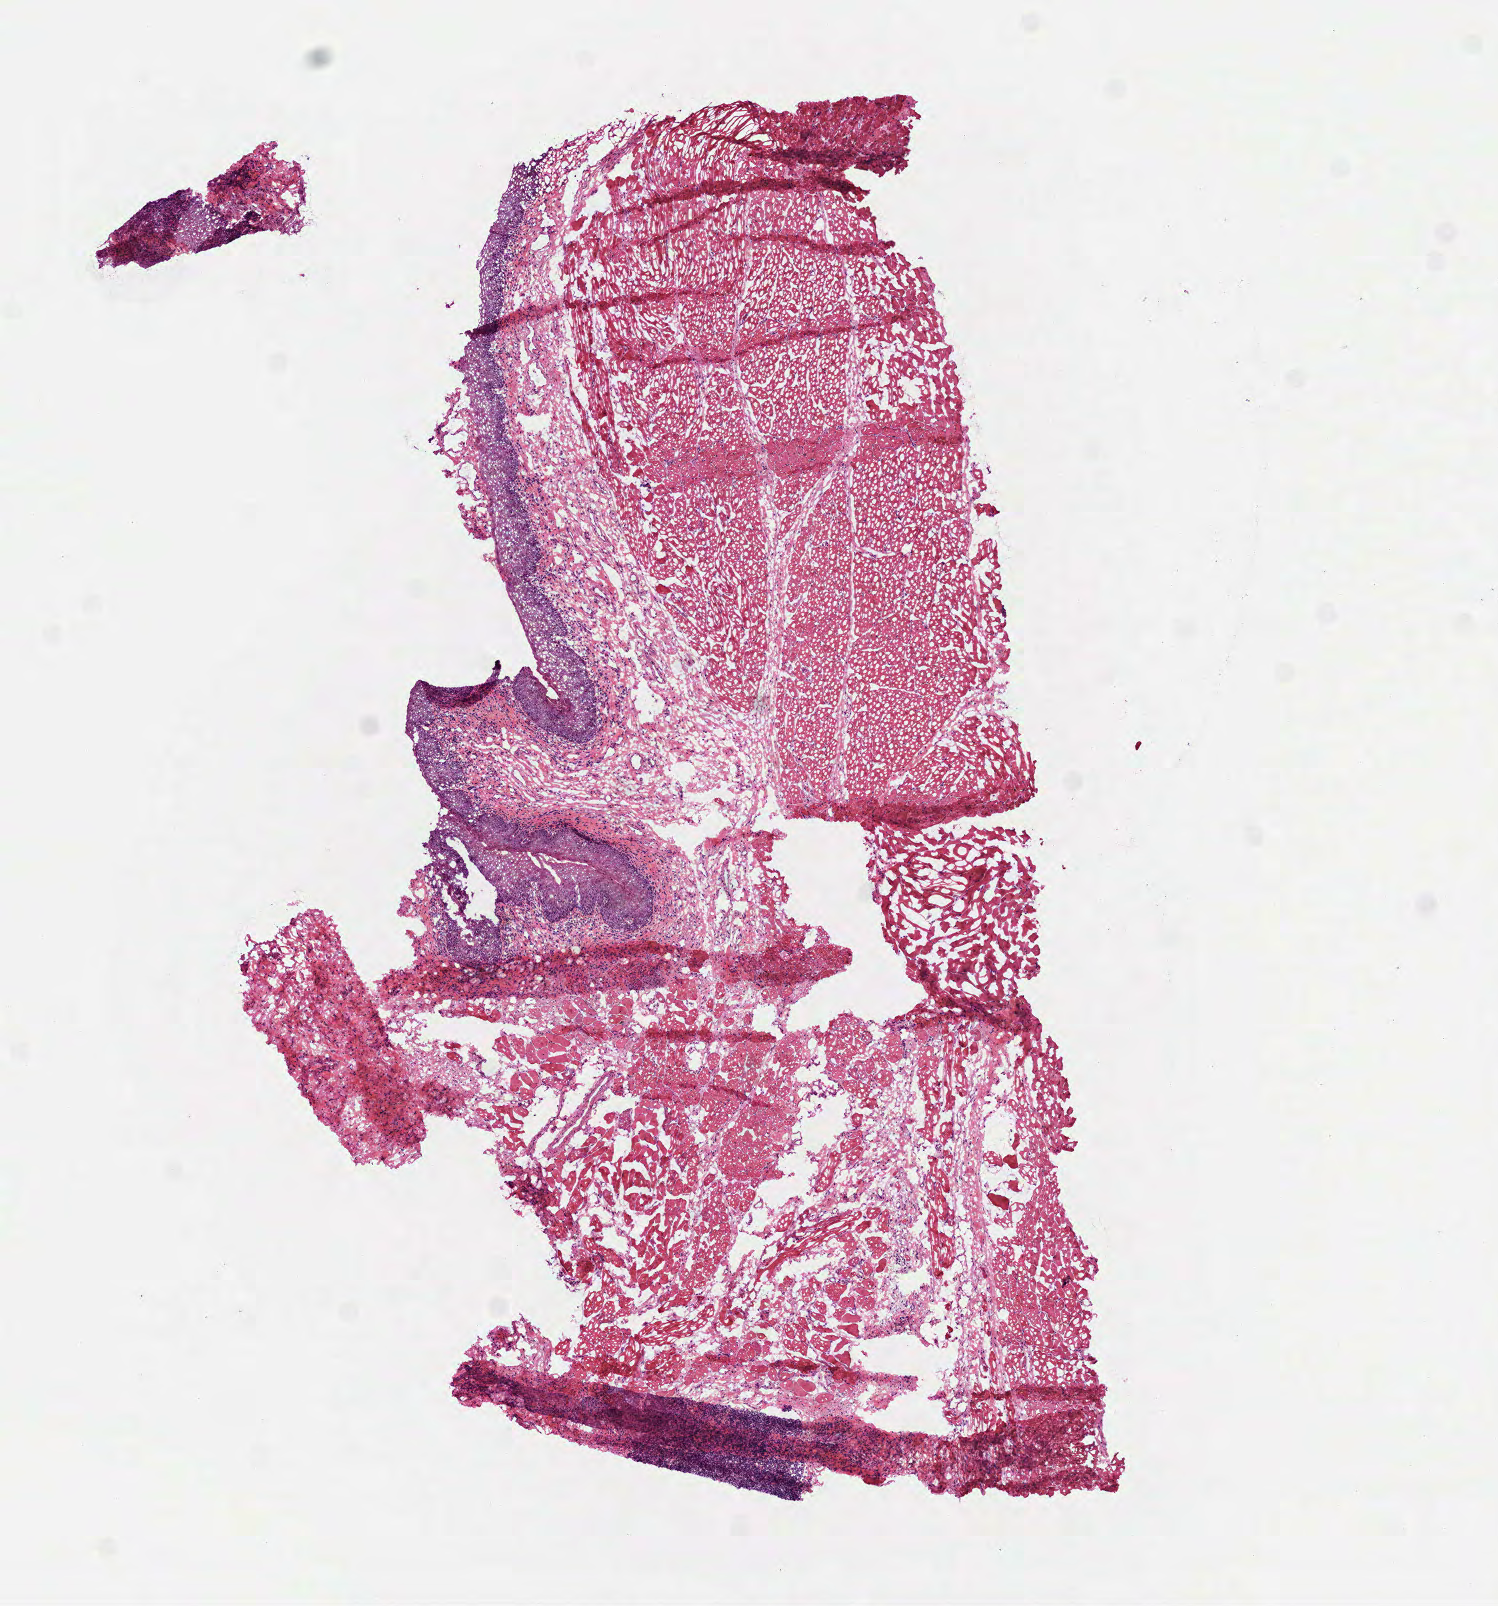
Digitized H&E-stained tissue section (whole slide) — whole scanned area (about 6.0 x 6.5 mm, acquisition: 40x scan) shown as a low-resolution overview. Frozen section from the top of the tissue portion. Solid tissue normal (non-tumour tissue) sample from the head and neck. Male, age 64 years at initial diagnosis.
• this section: solid tissue normal (non-tumour) sample from the same patient
• patient diagnosis: Squamous cell carcinoma, NOS